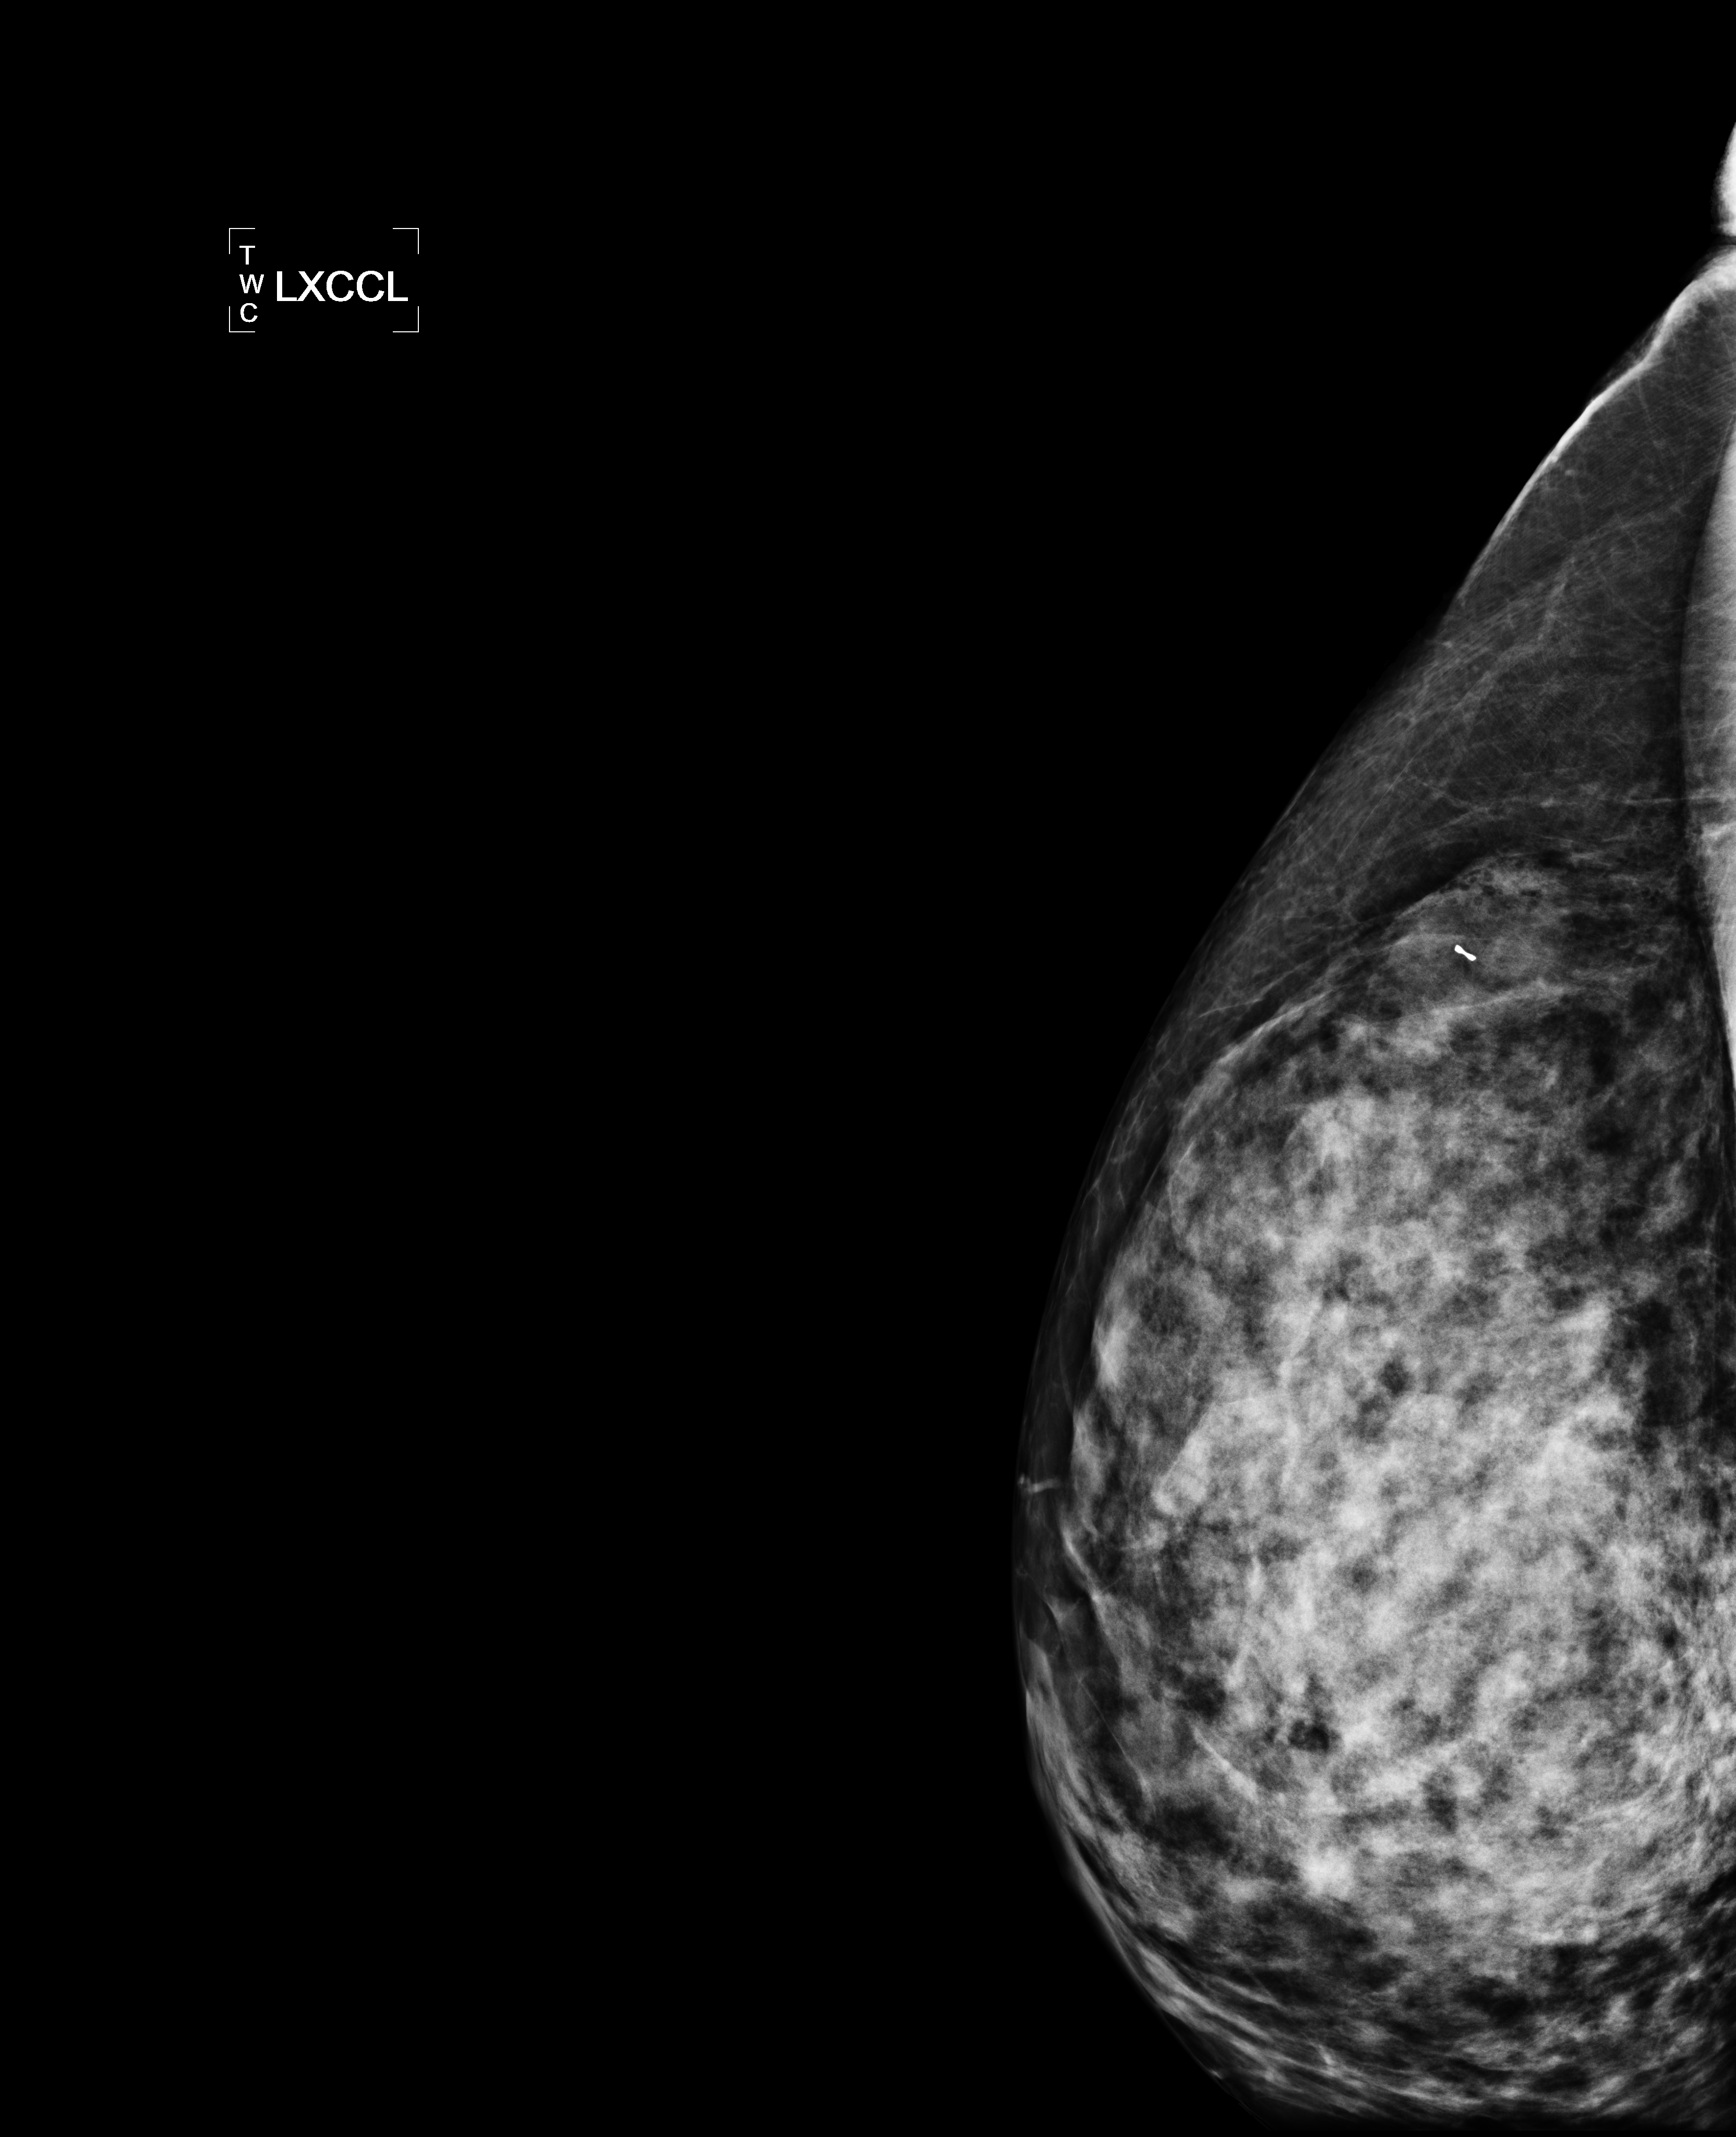
Diagnostic work-up study, system: Lorad Selenia. Female patient, age 43 years.
Image type: full-field digital mammogram. Breast: left. Projection: laterally exaggerated craniocaudal (XCCL) view.